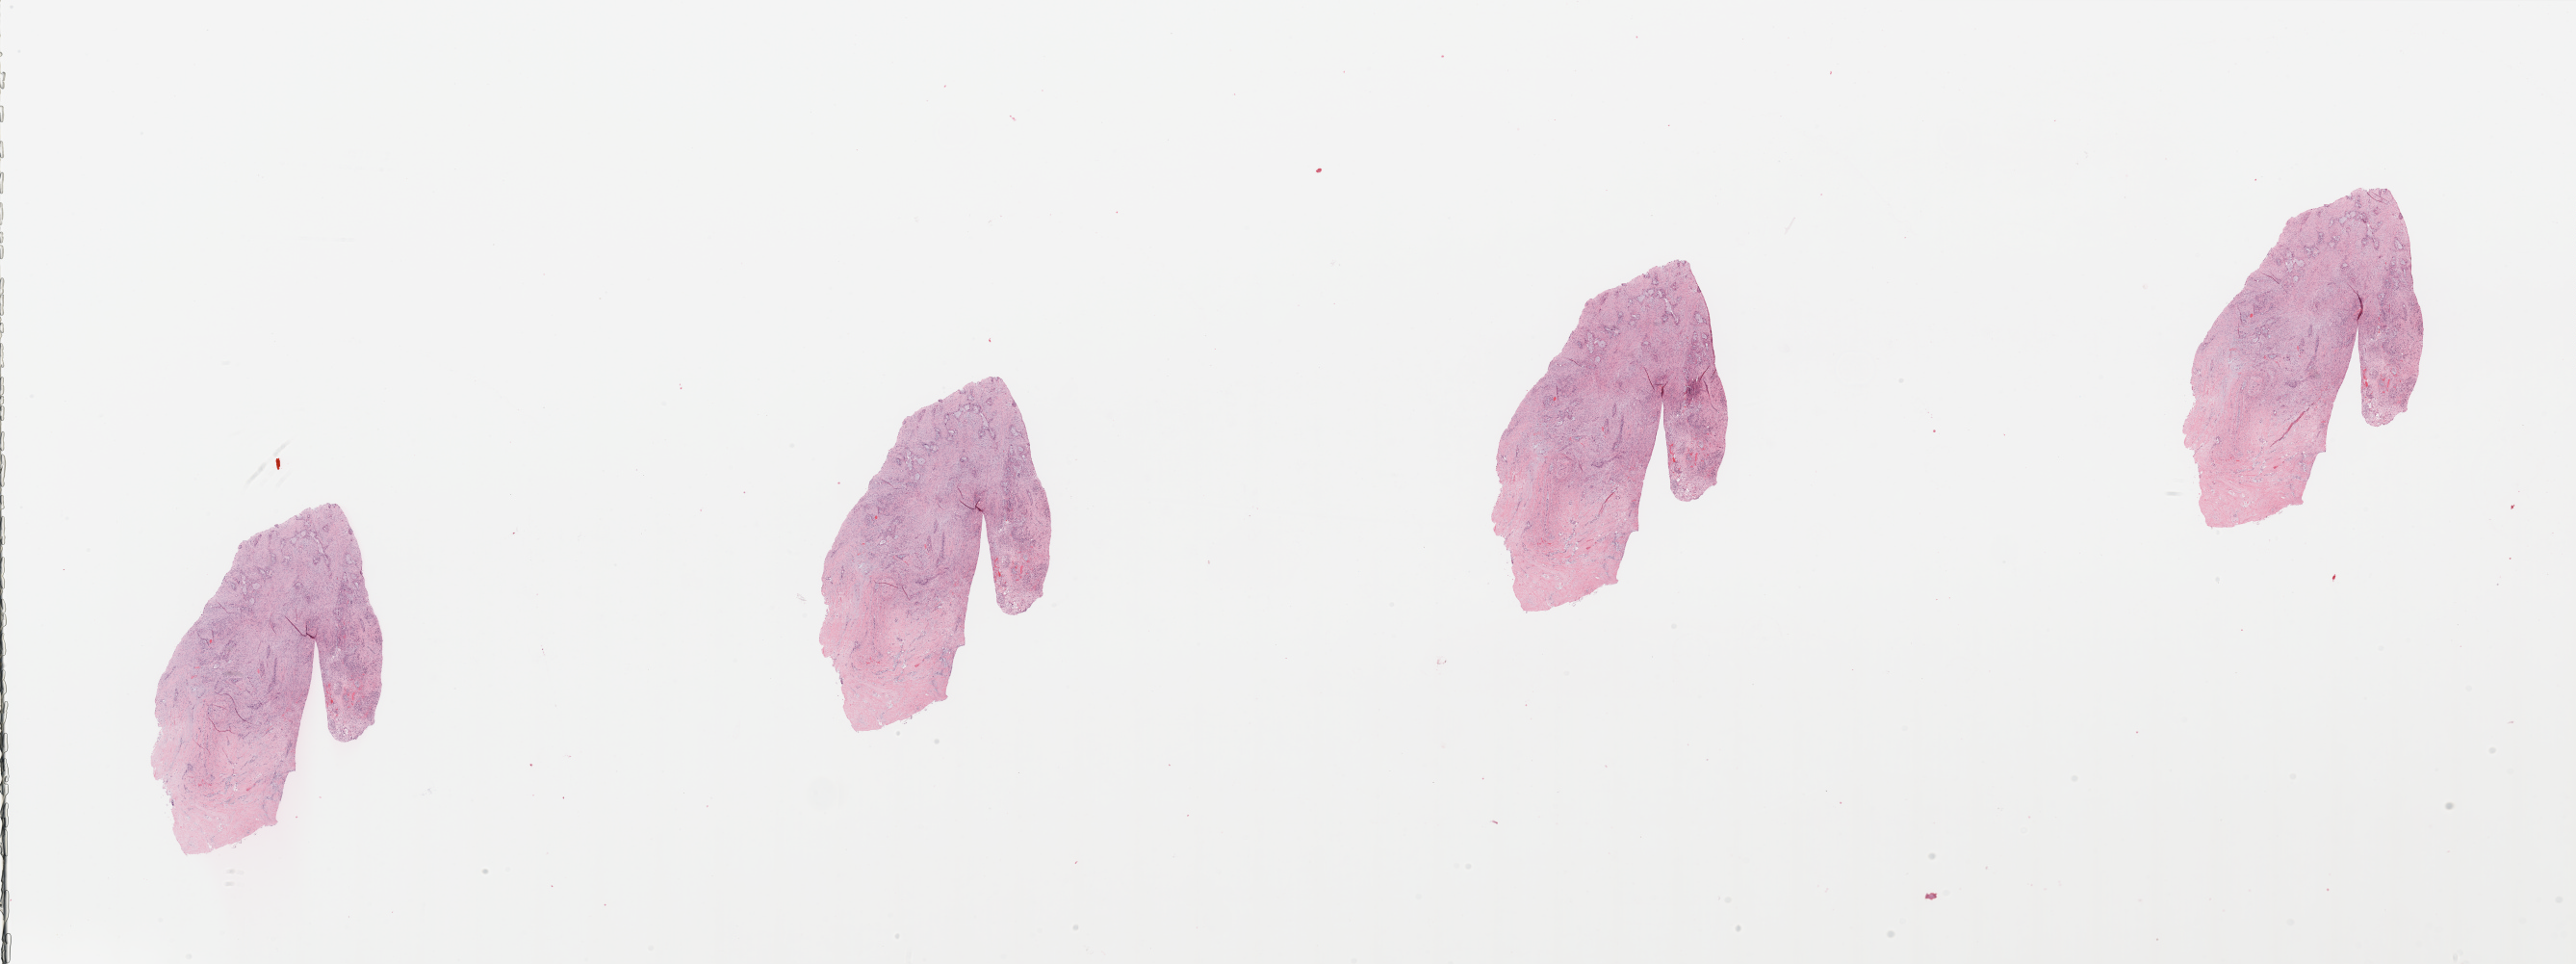
Digitized H&E tissue section (whole slide), shown as a low-resolution overview of the whole scanned area (about 42.3 x 15.8 mm, acquisition: 20x scan). Pancreas, tumour tissue. Patient: female, age 68 years. Histologic grade: G2 (moderately differentiated).
• AJCC pathologic stage: IIB
• primary tumour site (as recorded): head
• histologic diagnosis: Infiltrating duct carcinoma, NOS